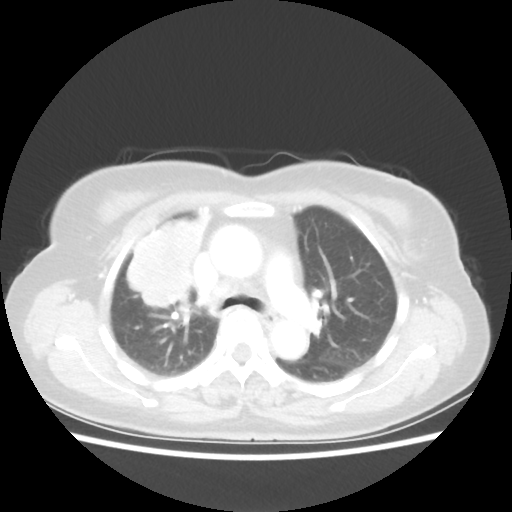
Chest CT, one axial slice; slice 36 of 55 in the series (ordered by position); reconstruction kernel STANDARD; lung window (W 1500 / L -600 HU); 5 mm slice thickness; 512 × 512 image matrix, field of view 337 × 337 mm. Female patient, age 62 years. From the clinical record (not read from this slice): clinical TNM (as recorded): T4 N3 M0.
Structures marked on this image (rectangle marked by the reading radiologist):
- lung tumour (recorded histology: squamous cell carcinoma): bounding box <116,206,216,312> (left, top, right, bottom; pixels)